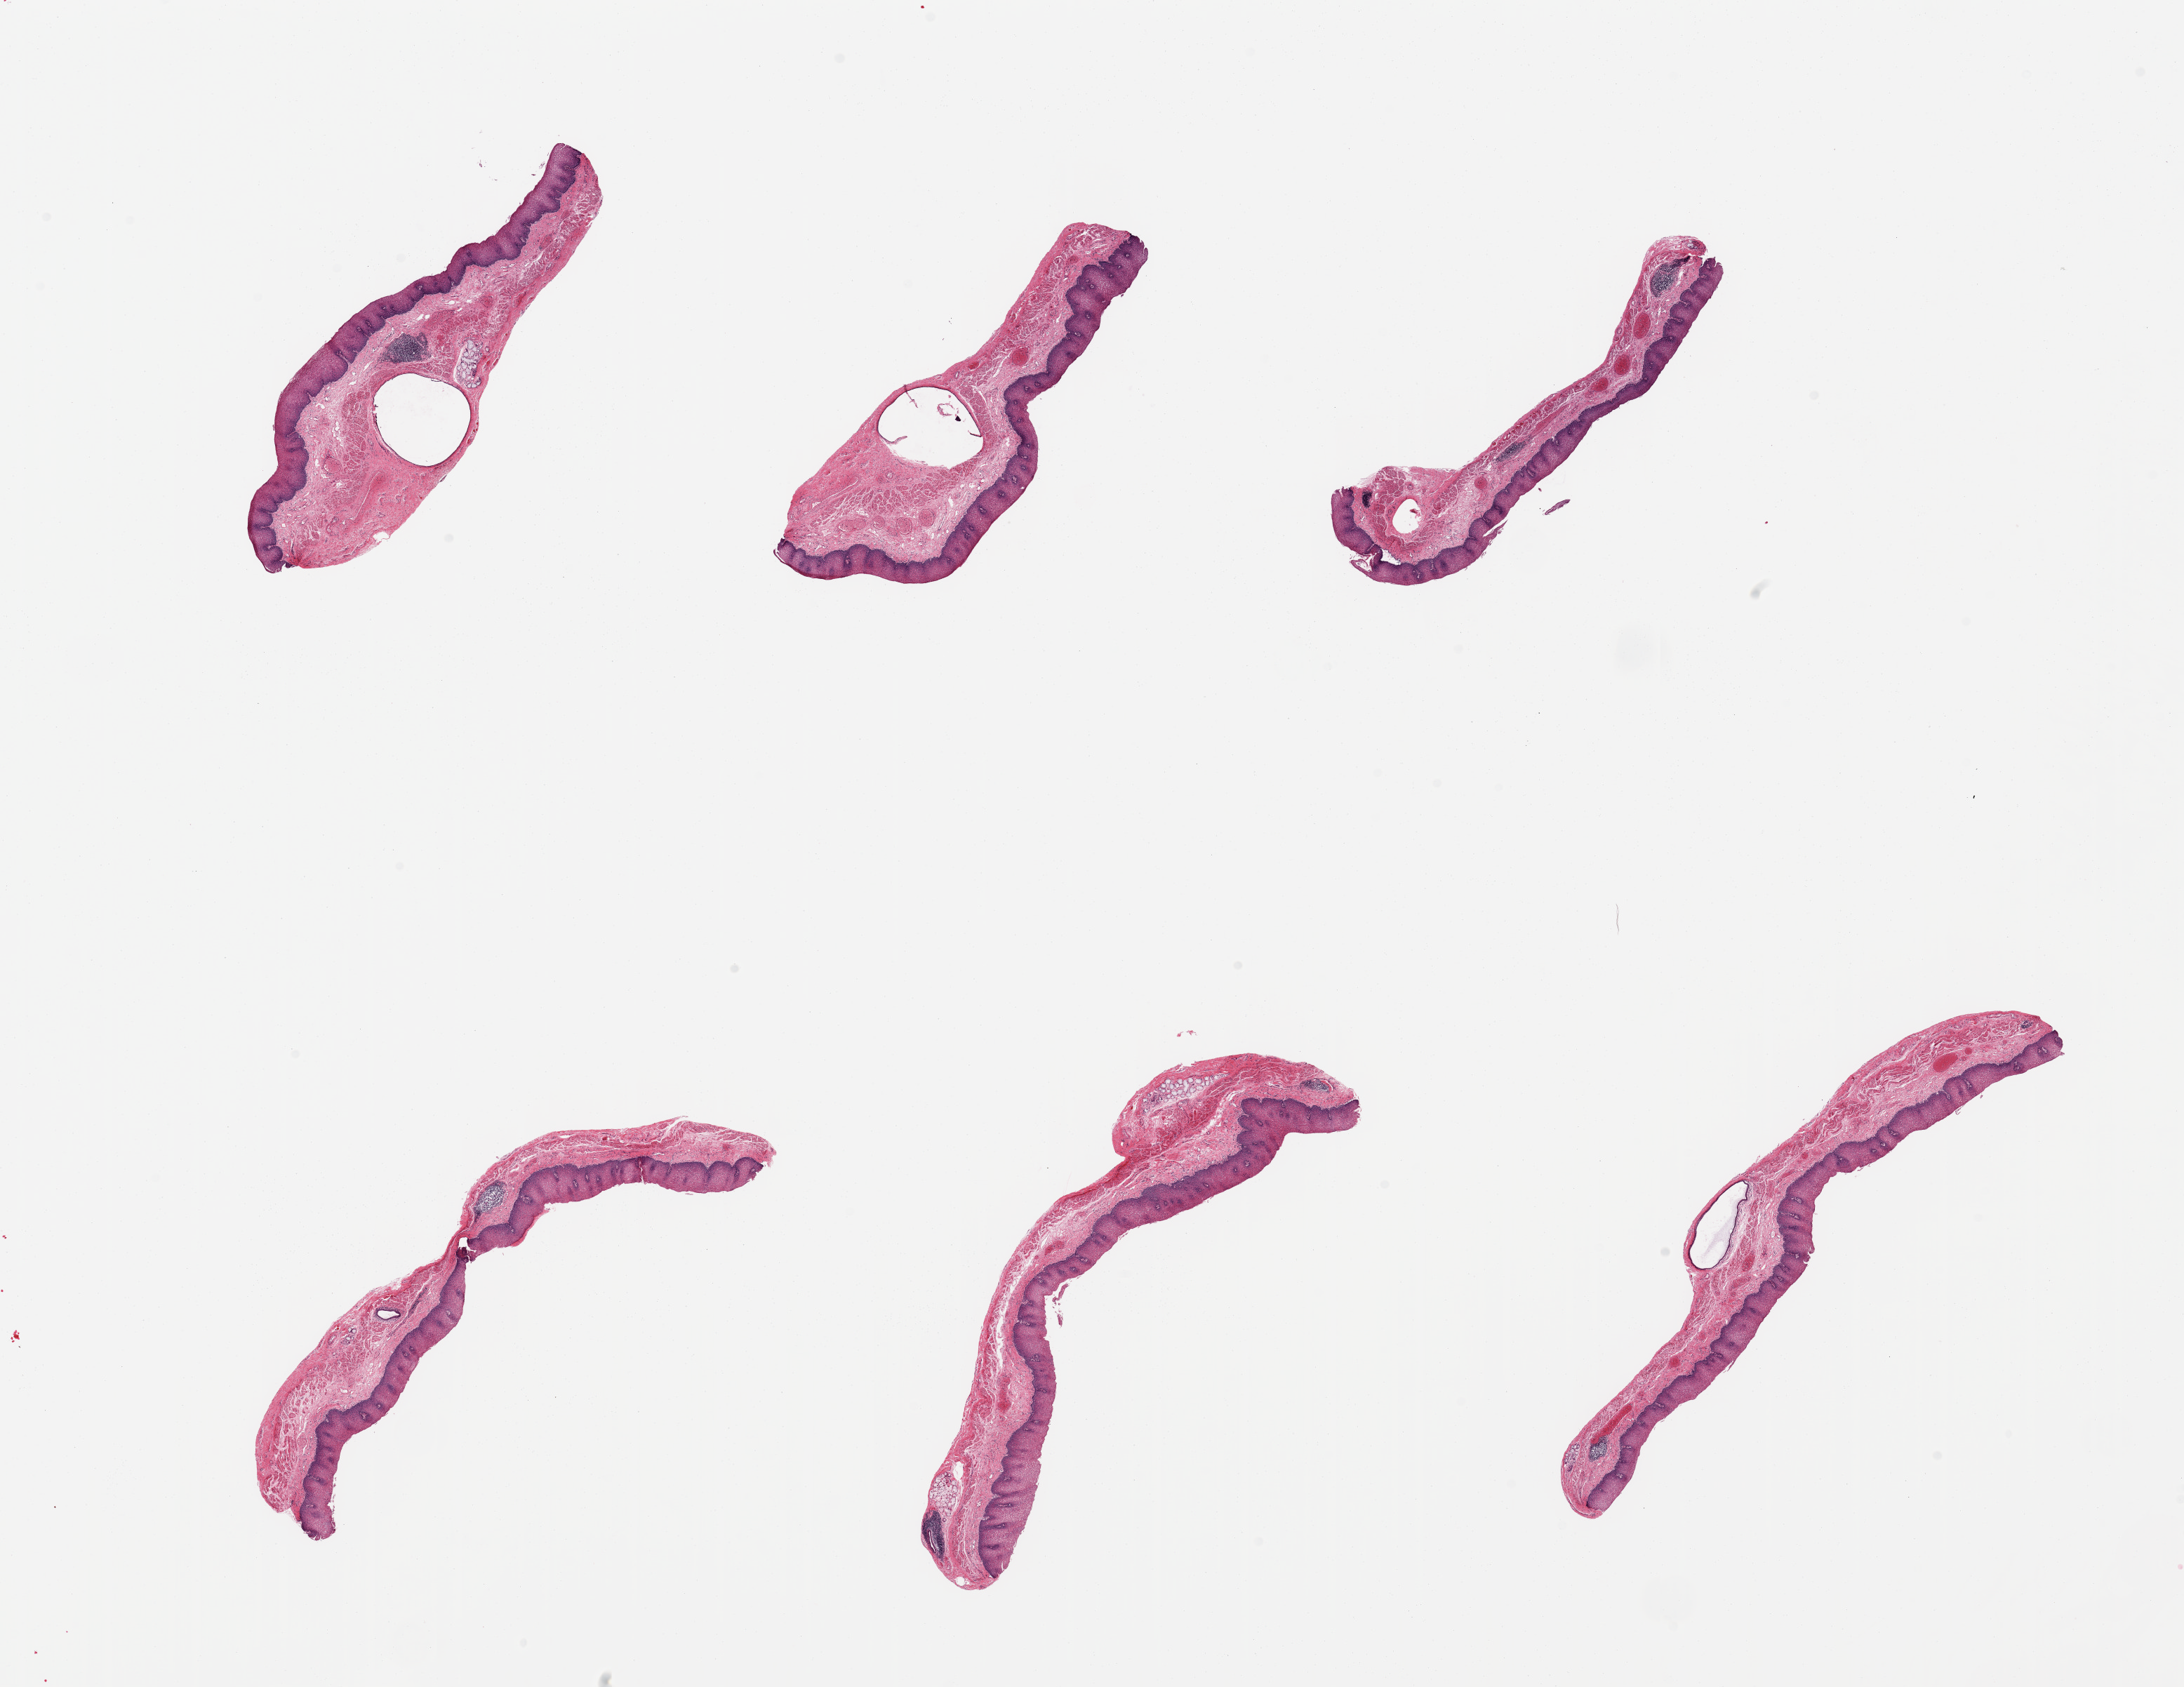
Whole-slide image, hematoxylin and eosin (H&E) stain, brightfield, whole scanned area (about 24.6 x 19.0 mm) shown as a low-resolution overview, PAXgene-fixed paraffin-embedded (PFPE) section, target tissue: esophageal mucous membrane, tissue donor sample. Donor: male.
Pathologist's review note for this sample: 6 pieces; squamous mucosa ~0.3mm, submucosal mucus glands present.